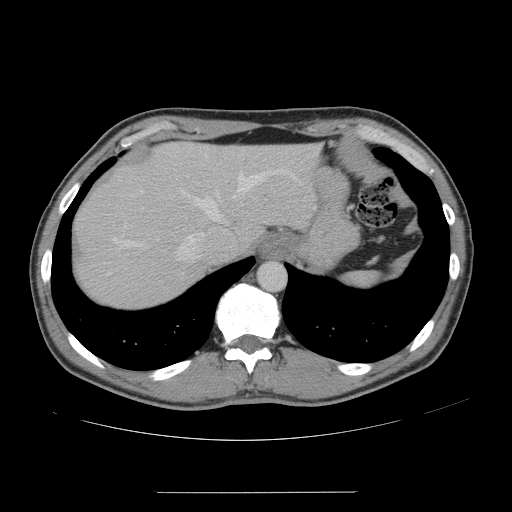
Contrast-enhanced abdominal CT, one axial slice. Position 125 of 178 along the scan axis. 120 kVp. Intravenous contrast given. Soft-tissue window (W 400 / L 40 HU). 512 × 512 image matrix, field of view 401 × 401 mm. Male patient, age 53 years. From the clinical record (not read from this slice): diagnosis: colorectal cancer liver metastases, imaged before liver resection; multiple liver metastases: yes; largest metastasis: 2.4 cm; disease in both lobes: no.
Annotated regions visible in this slice (manually delineated by an expert):
- hepatic veins: box from (x=113, y=169) to (x=297, y=261) px
- liver: (x=75, y=143)–(x=319, y=308)
- planned liver remnant (the part of the liver to remain after resection): (x=156, y=142)–(x=319, y=243)